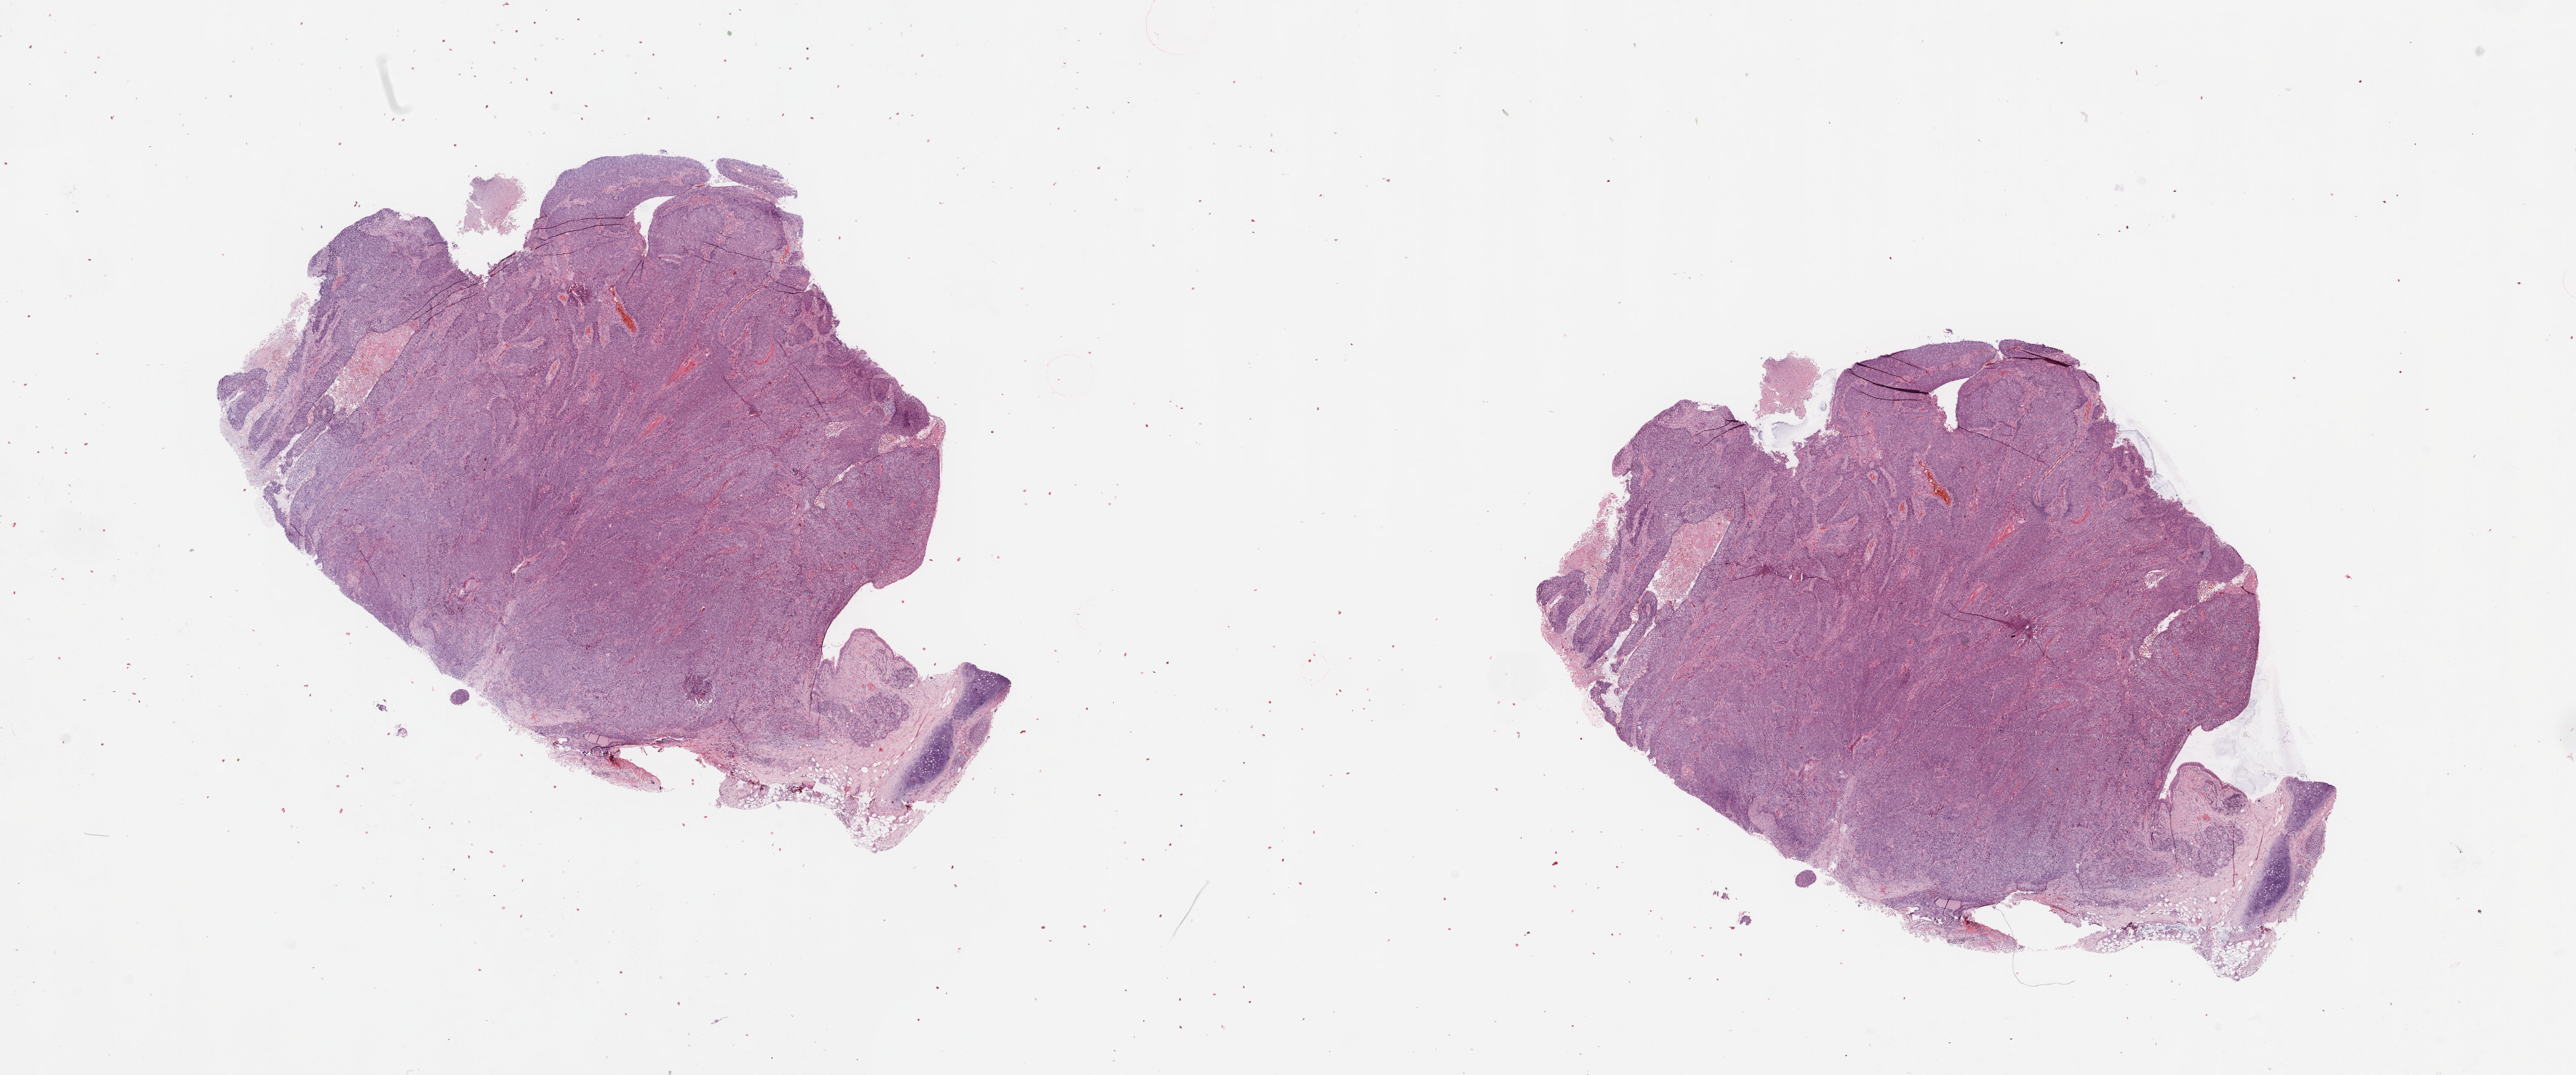
Digitized Hematoxylin and eosin (H&E) stained tissue section (whole slide) — shown as a low-resolution overview of the whole scanned area (about 28.5 x 11.9 mm, from a 20x scan), tumour tissue sample, sampled site: lung. Patient: male, age 65 years.
Diagnosis: Squamous cell carcinoma, NOS.